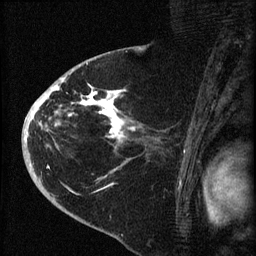
Breast MRI (dynamic contrast-enhanced), one sagittal slice; slice 42 of 60 in the series (ordered by position); dynamic contrast-enhanced series, image 2 of 4 at this slice position (ordered by acquisition); 1.5 T; TE 4.2 ms, TR 8.2 ms; 2 mm slice thickness; 256 × 256 image matrix, field of view 180 × 180 mm. Patient: female, 71 years.
Outlined on this slice (semi-automatically segmented with operator editing):
- analysis volume of interest (the breast-tissue region the enhancement analysis was run in; not a lesion): bounding box (x1, y1, x2, y2) in pixels: (35, 75, 153, 190)
- tumour enhancement mask (voxels above the 70 % enhancement threshold inside the analysis volume of interest): (35, 79, 136, 179)